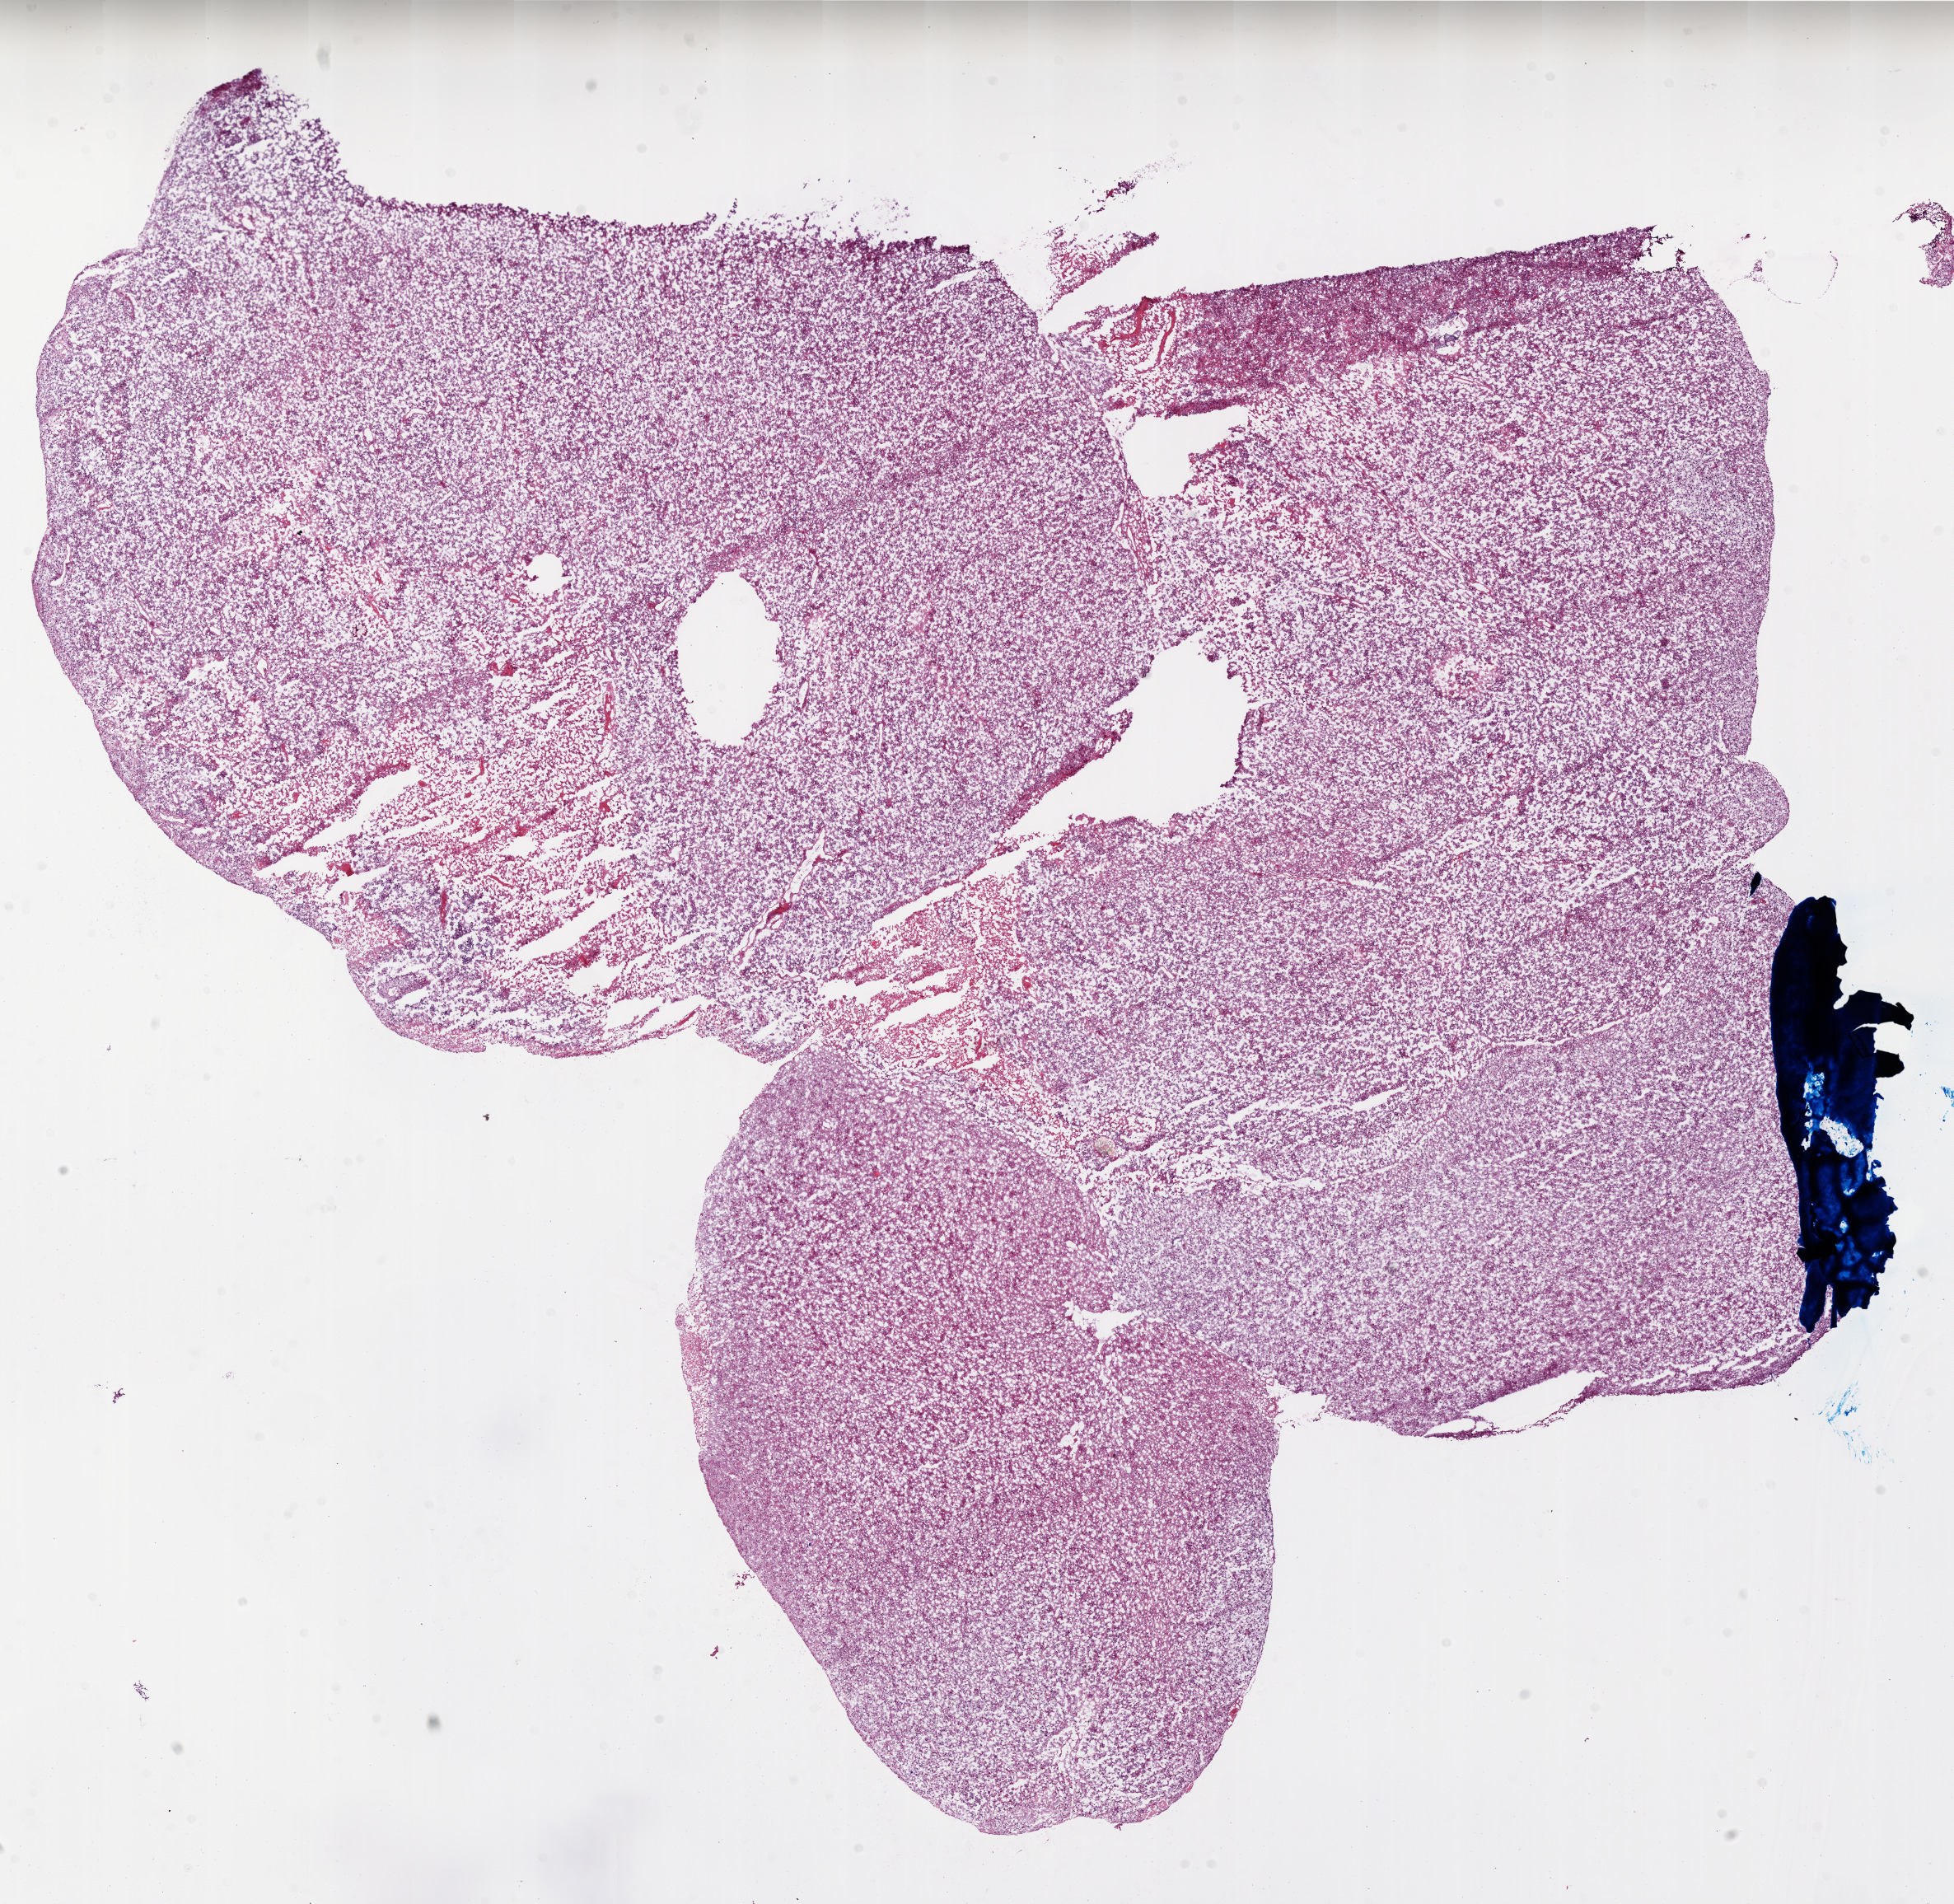
Digitized H&E-stained tissue section (whole slide), whole scanned area (about 19.0 x 18.5 mm, slide scanned at 20x) shown as a low-resolution overview; frozen section from the top of the tissue portion; brain, primary tumour sample. Patient: female, age at initial diagnosis 78 years. Composition of this section per pathologist review: tumour cells 90%, tumour nuclei 100%, normal cells 0%, stromal cells 0%, necrosis 10%. Infiltration values recorded for this section: lymphocyte infiltration 0%, monocyte infiltration 0%, neutrophil infiltration 0%.
Histologic diagnosis: Glioblastoma.